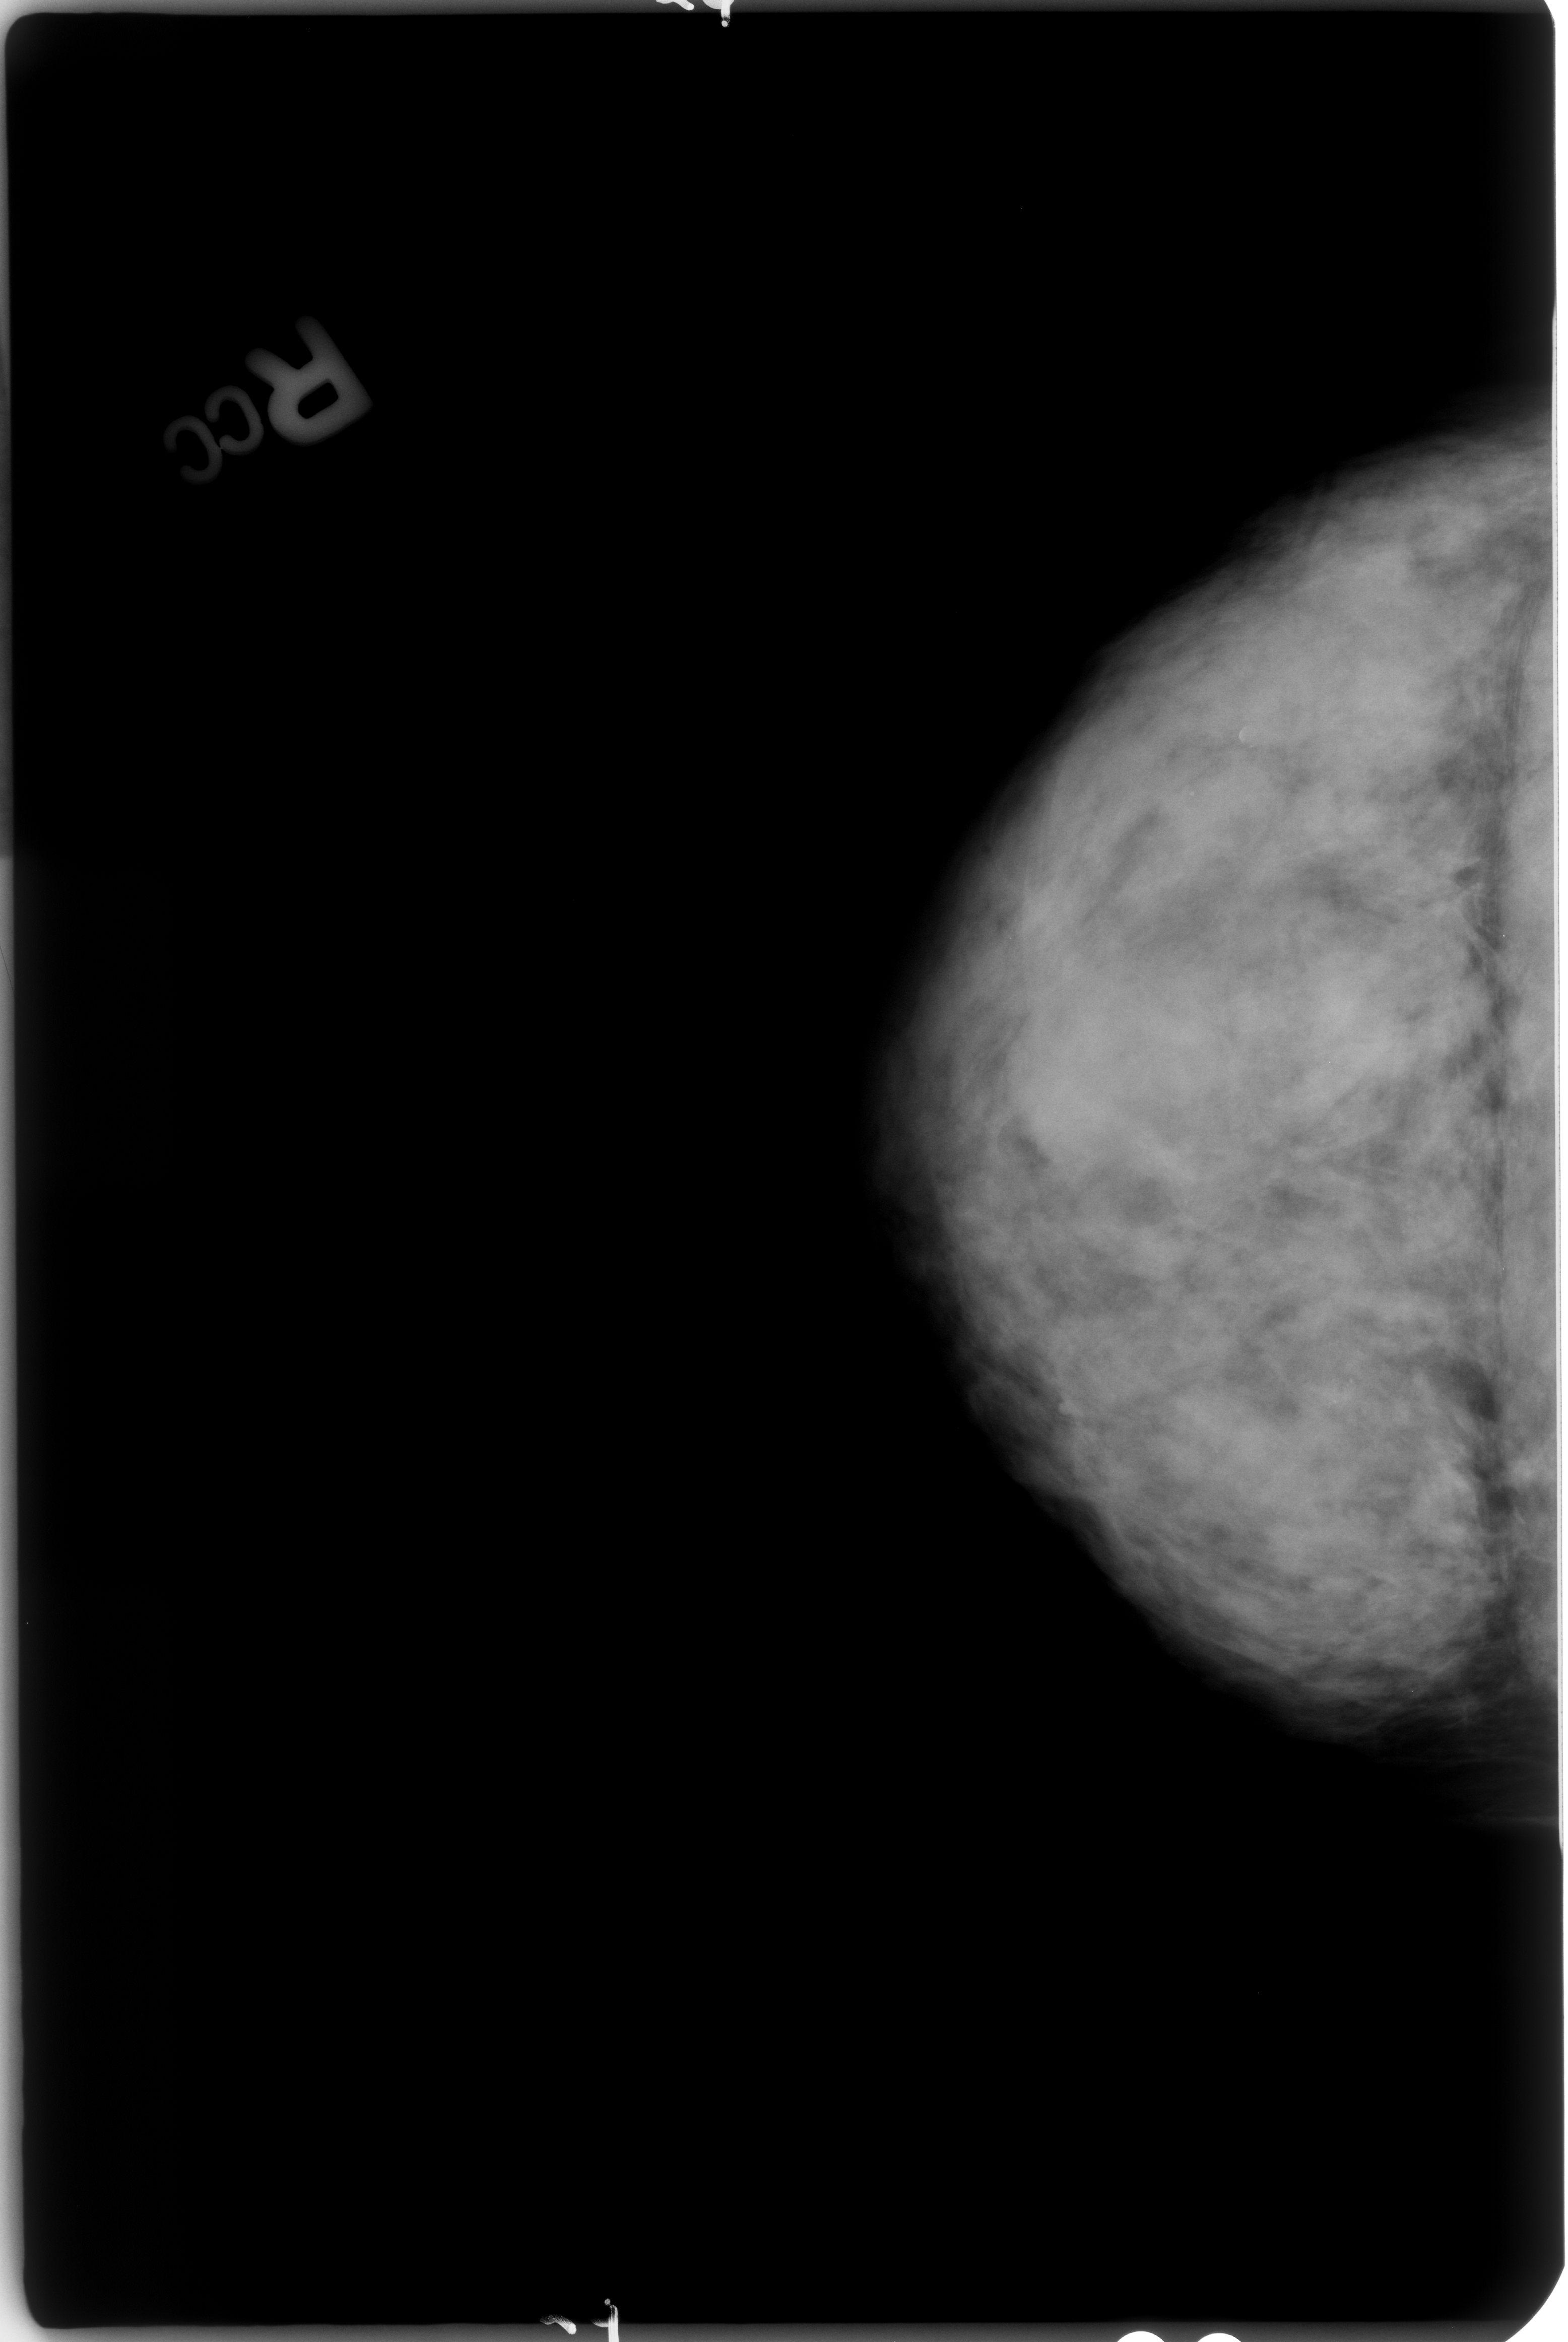
Scanned film-screen mammogram; right breast; CC view; BI-RADS breast density category 4 (scale 1–4).
Abnormality record for this image: calcifications, morphology lucent center; BI-RADS assessment category 2; benign; no additional work-up was recommended (benign without callback).